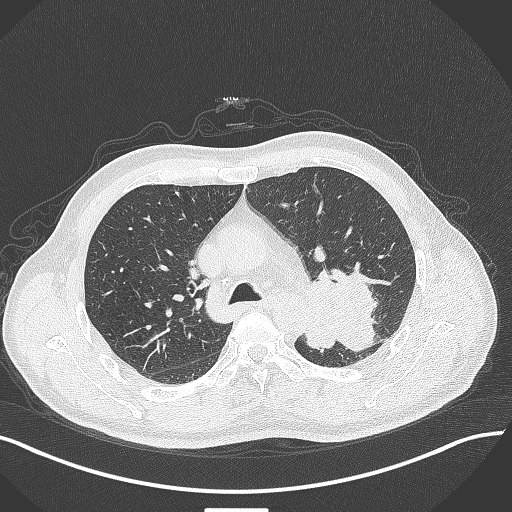
Chest CT, one axial slice. Slice 286 of 429 in the series (ordered by position). Reconstruction kernel B70f. 120 kVp. Lung window (W 1500 / L -600 HU). 1 mm slice thickness. 512 × 512 image matrix. Male patient, age 55 years. From the clinical record (not read from this slice): clinical TNM (as recorded): T3 N0 M1c.
Outlined on this slice (rectangle marked by the reading radiologist):
- lung tumour (recorded histology: adenocarcinoma): bounding box [x1, y1, x2, y2] px = [300, 264, 381, 353]